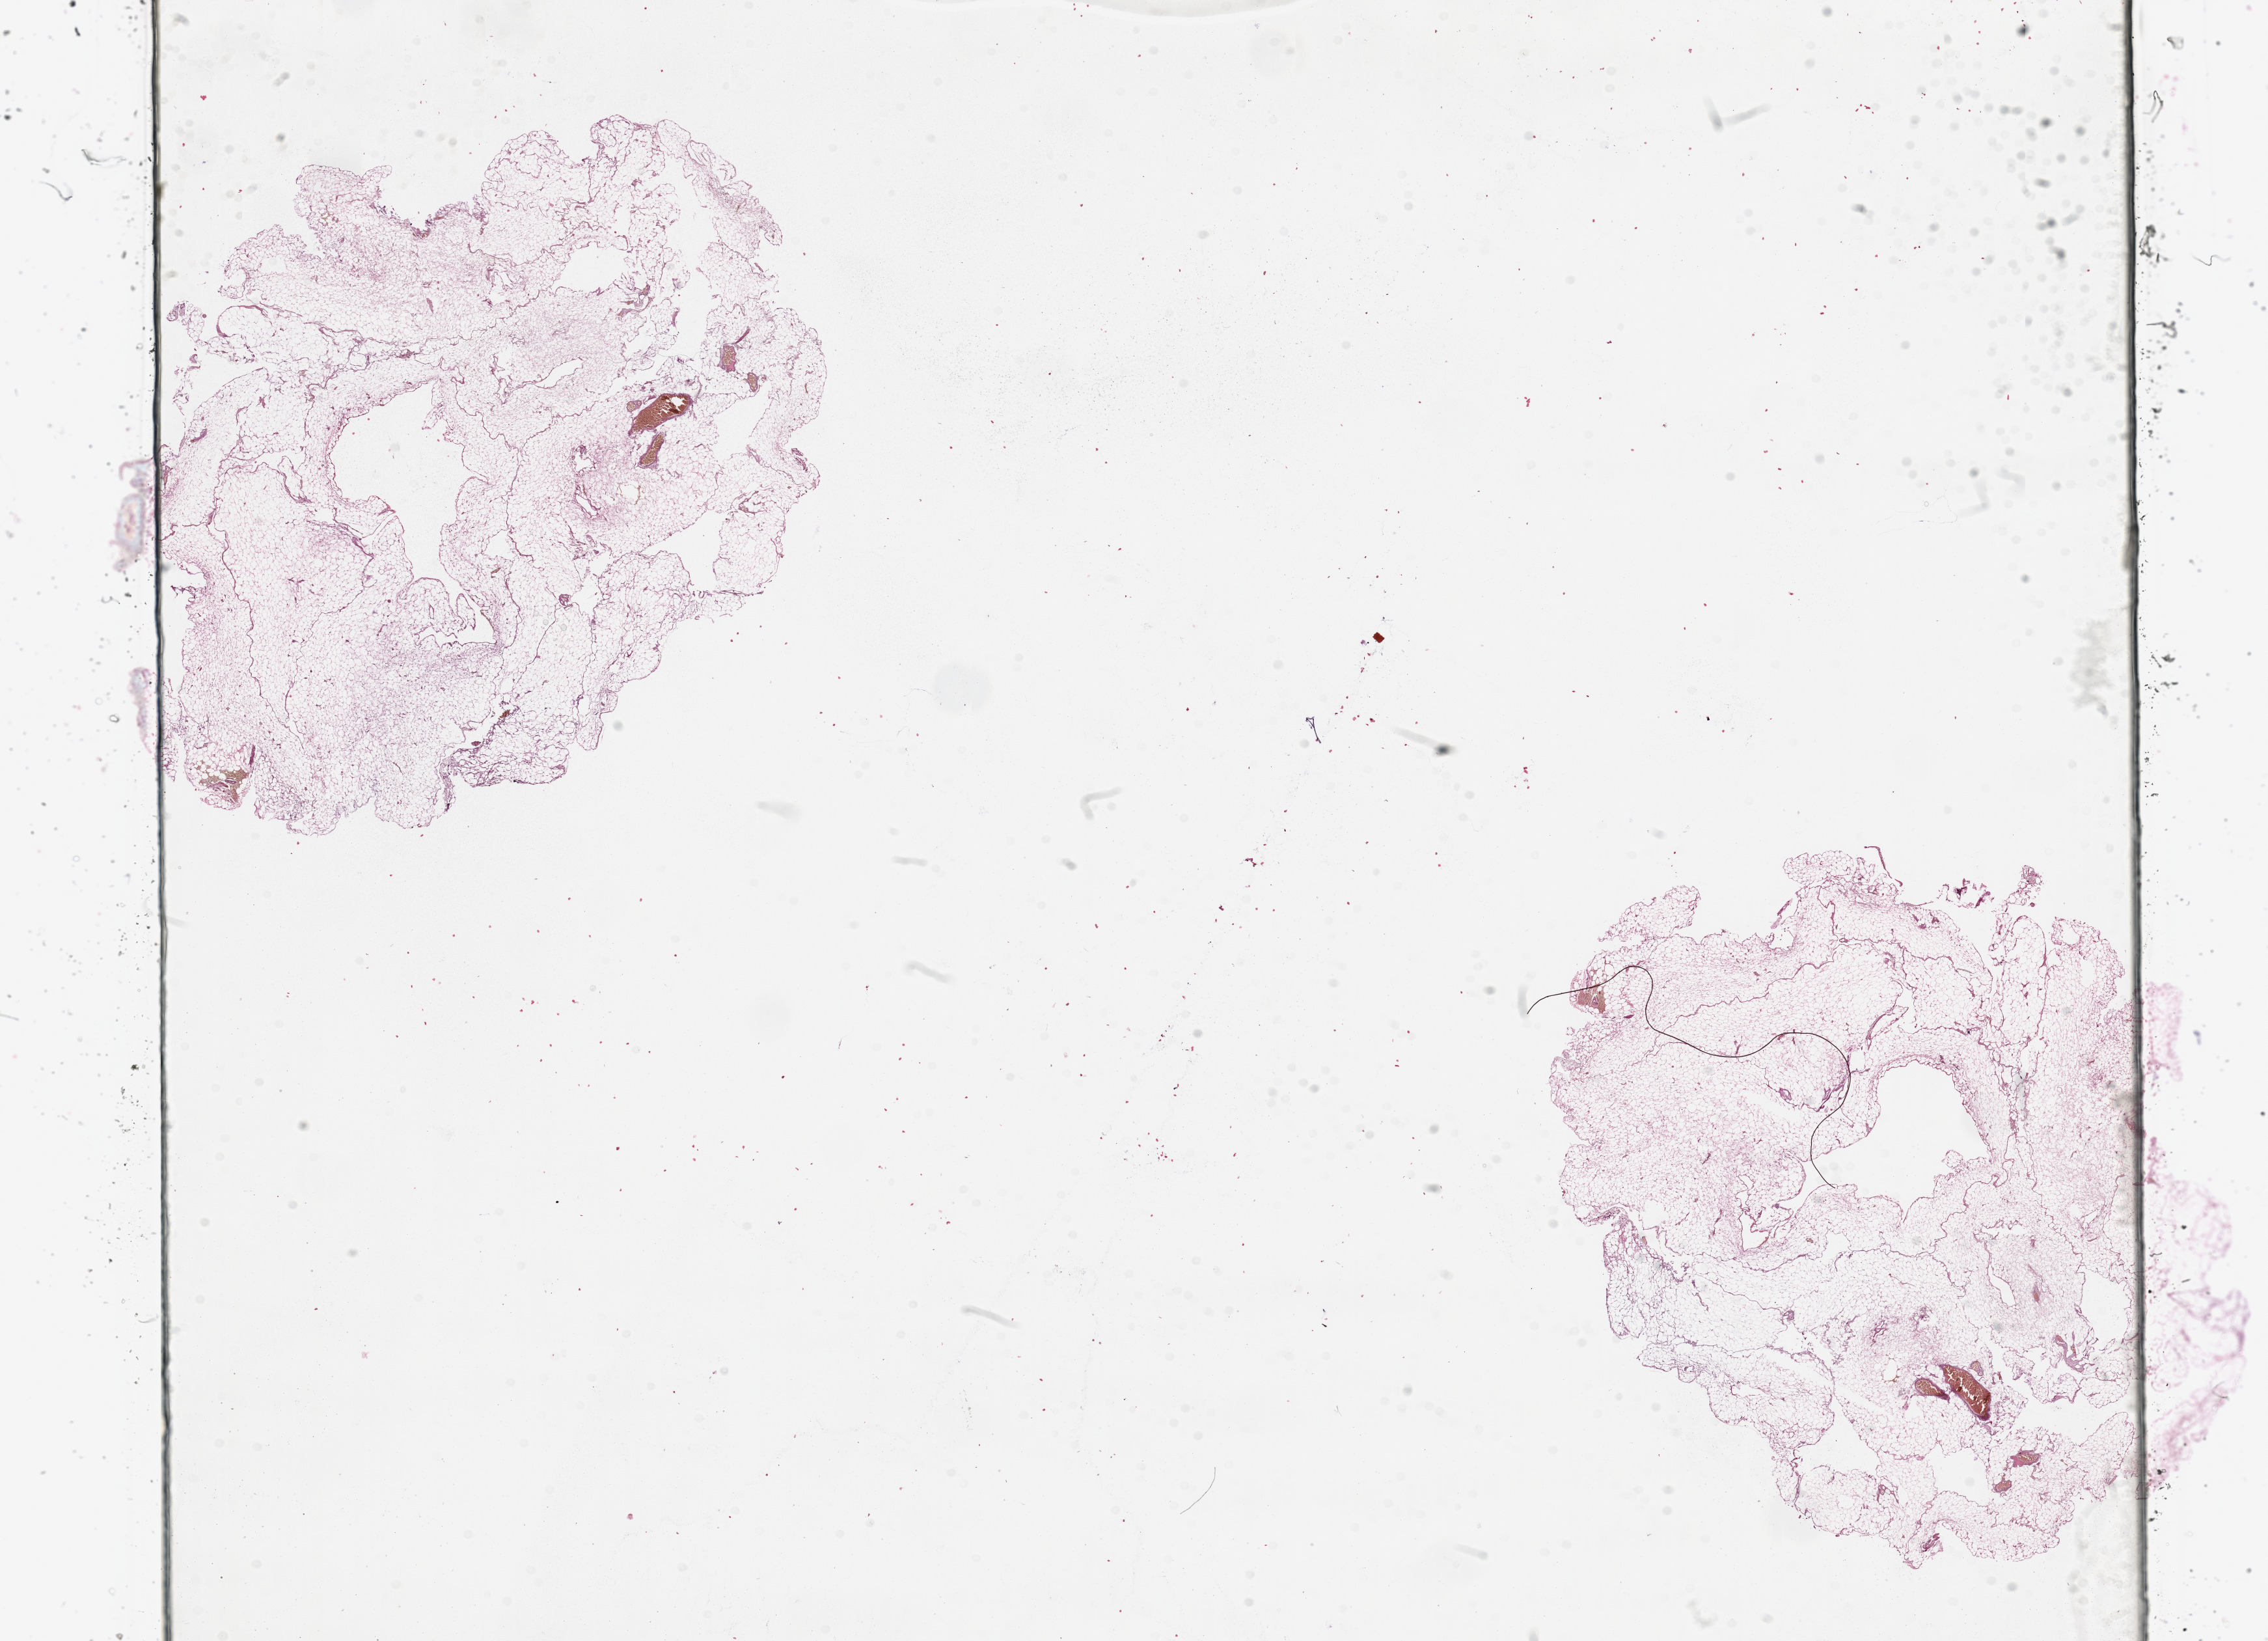
Digitized H&E tissue section (whole slide), whole scanned area (about 27.6 x 19.9 mm) shown as a low-resolution overview, normal (non-tumour) tissue sample. Patient: male, age 53 years.
* this section: normal (non-tumour) tissue from the same patient
* patient diagnosis (cohort enrolment): sarcoma (site not recorded at cohort level)